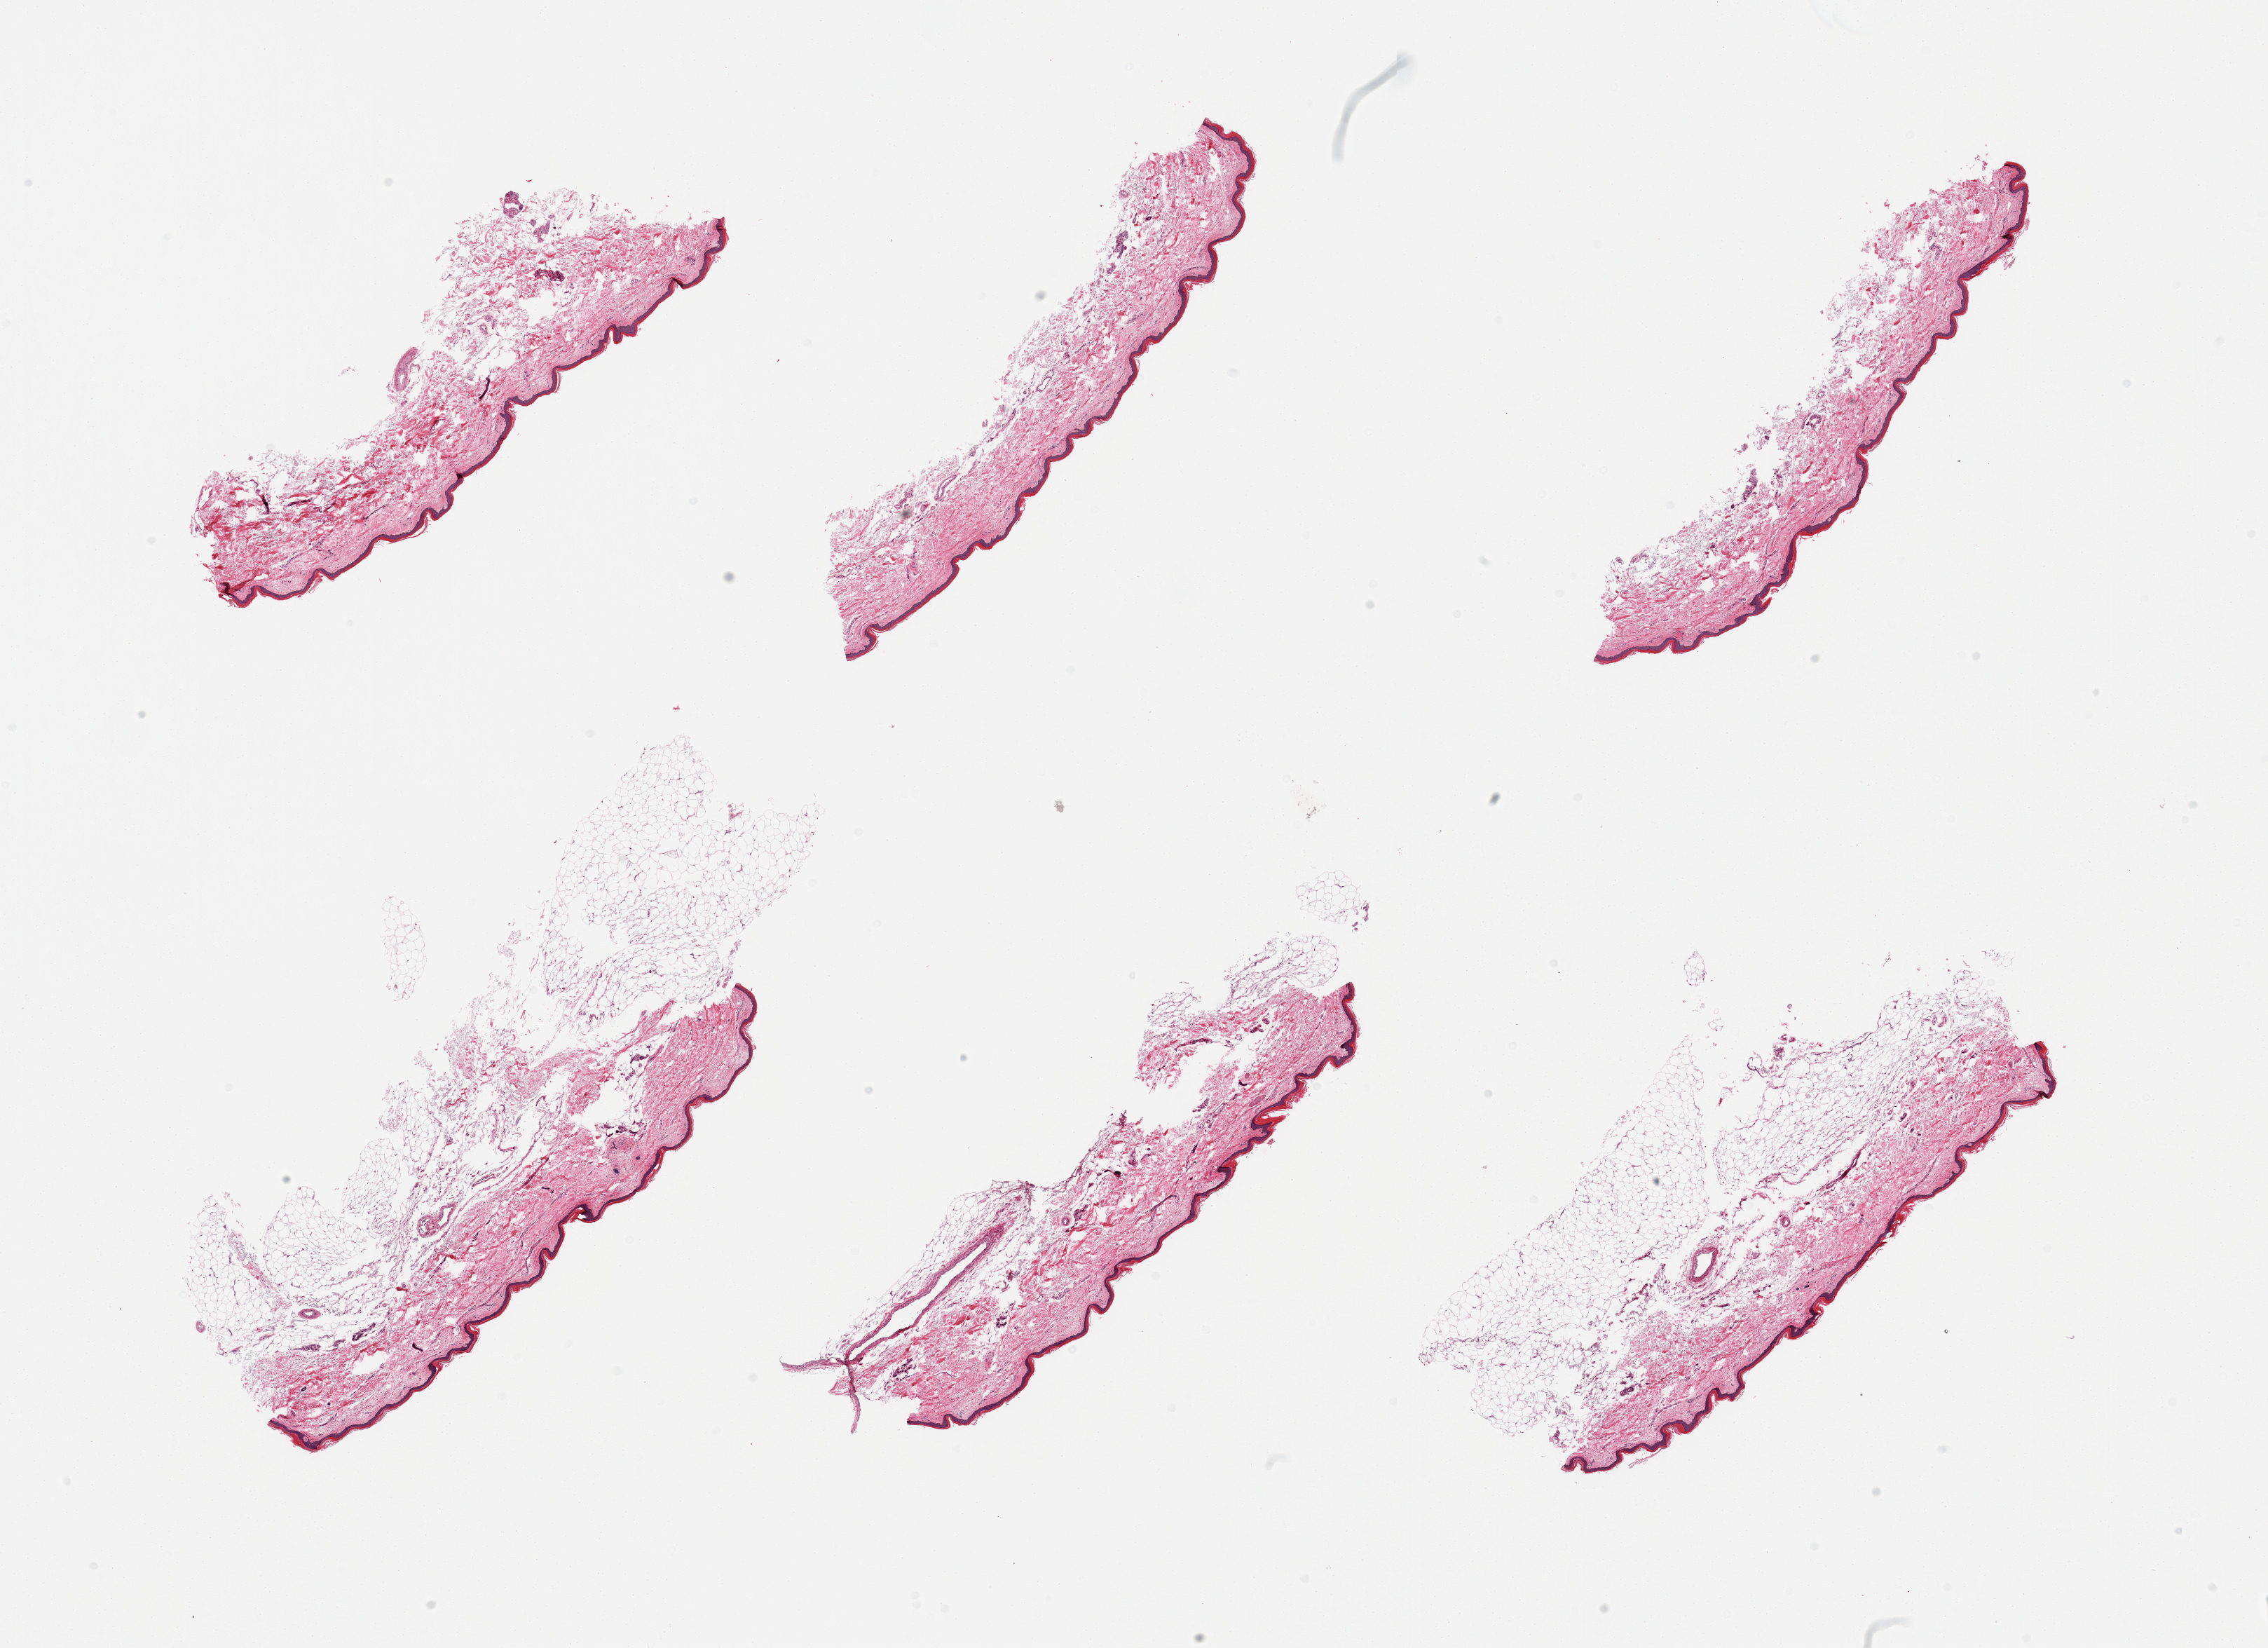
Hematoxylin and eosin (H&E) whole-slide image, a low-resolution overview of the entire scanned area, about 25.6 x 18.6 mm. PAXgene-fixed paraffin-embedded (PFPE) section. Section of skin of lower leg (target tissue). Tissue donor sample. Donor sex: female.
Pathologist's review note for this sample: 6 pieces; poorly trimmed, up to 2 mm subcutaneous fat.